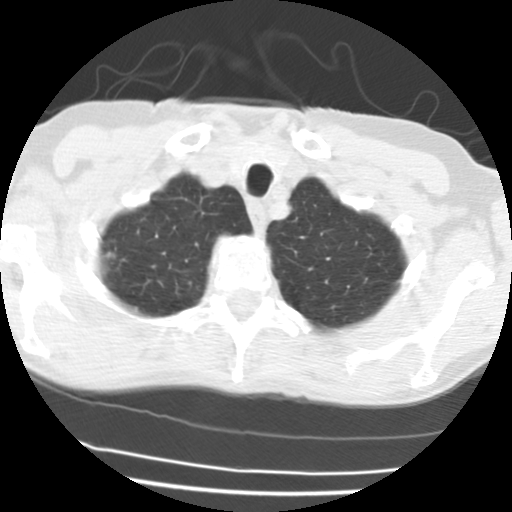
Chest CT (low-dose screening protocol), one axial image; third annual screen; lung window (W 1500 / L -600 HU); 2.5 mm slice thickness; 120 kVp. Female participant, aged 58 years at enrolment. Current smoker at enrolment.
Expert reader's lesion annotation, bounding box <86,241,129,275> (left, top, right, bottom; pixels). The screening reader recorded 3 non-calcified nodules or masses ≥4 mm on this exam (right upper lobe, left upper lobe, right upper lobe); which of them this box marks is not recorded. Official screen result: positive, other. Lung cancer was diagnosed 153 days after this screen: bronchiolo-alveolar adenocarcinoma, NOS, right upper lobe, well differentiated (G1), stage IA (AJCC 6th edition), 8 mm at pathology.